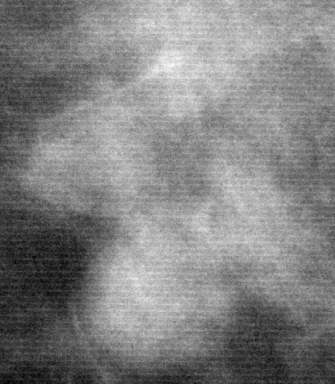
Crop from a digitized film mammogram around one marked abnormality; right breast; CC view; BI-RADS breast density category 2 (scale 1–4).
- Marked abnormality: mass, shape round, margins circumscribed; BI-RADS assessment category 3; pathology result (as recorded, not read from the image): benign.